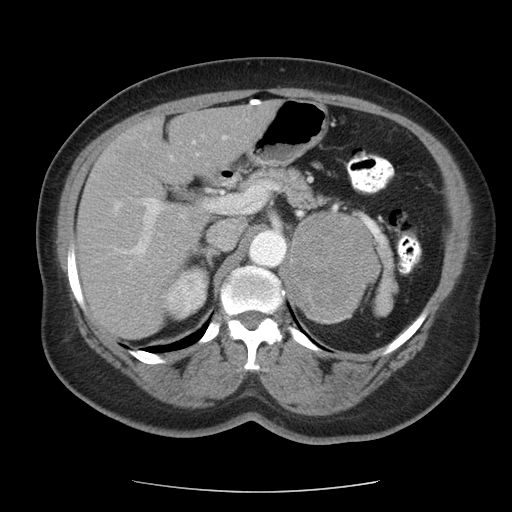
Contrast-enhanced abdominal CT, one axial slice. Slice 68 of 95 in the series (ordered by position). Reconstruction kernel STANDARD. 120 kVp. Intravenous contrast given. Soft-tissue window (W 400 / L 40 HU). 5 mm slice thickness. 512 × 512 image matrix, field of view 362 × 362 mm. Patient: female, 71 years. From the clinical record (not read from this slice): diagnosis: adrenocortical carcinoma; tumour side: left adrenal; tumour size at pathology: 8.8 cm; Ki-67 index: 20 %; stage (as recorded): 2.
Structures marked on this image (semi-automatic segmentation, software-assisted and operator-edited):
- mass: bounding box <287,211,379,322> (left, top, right, bottom; pixels)